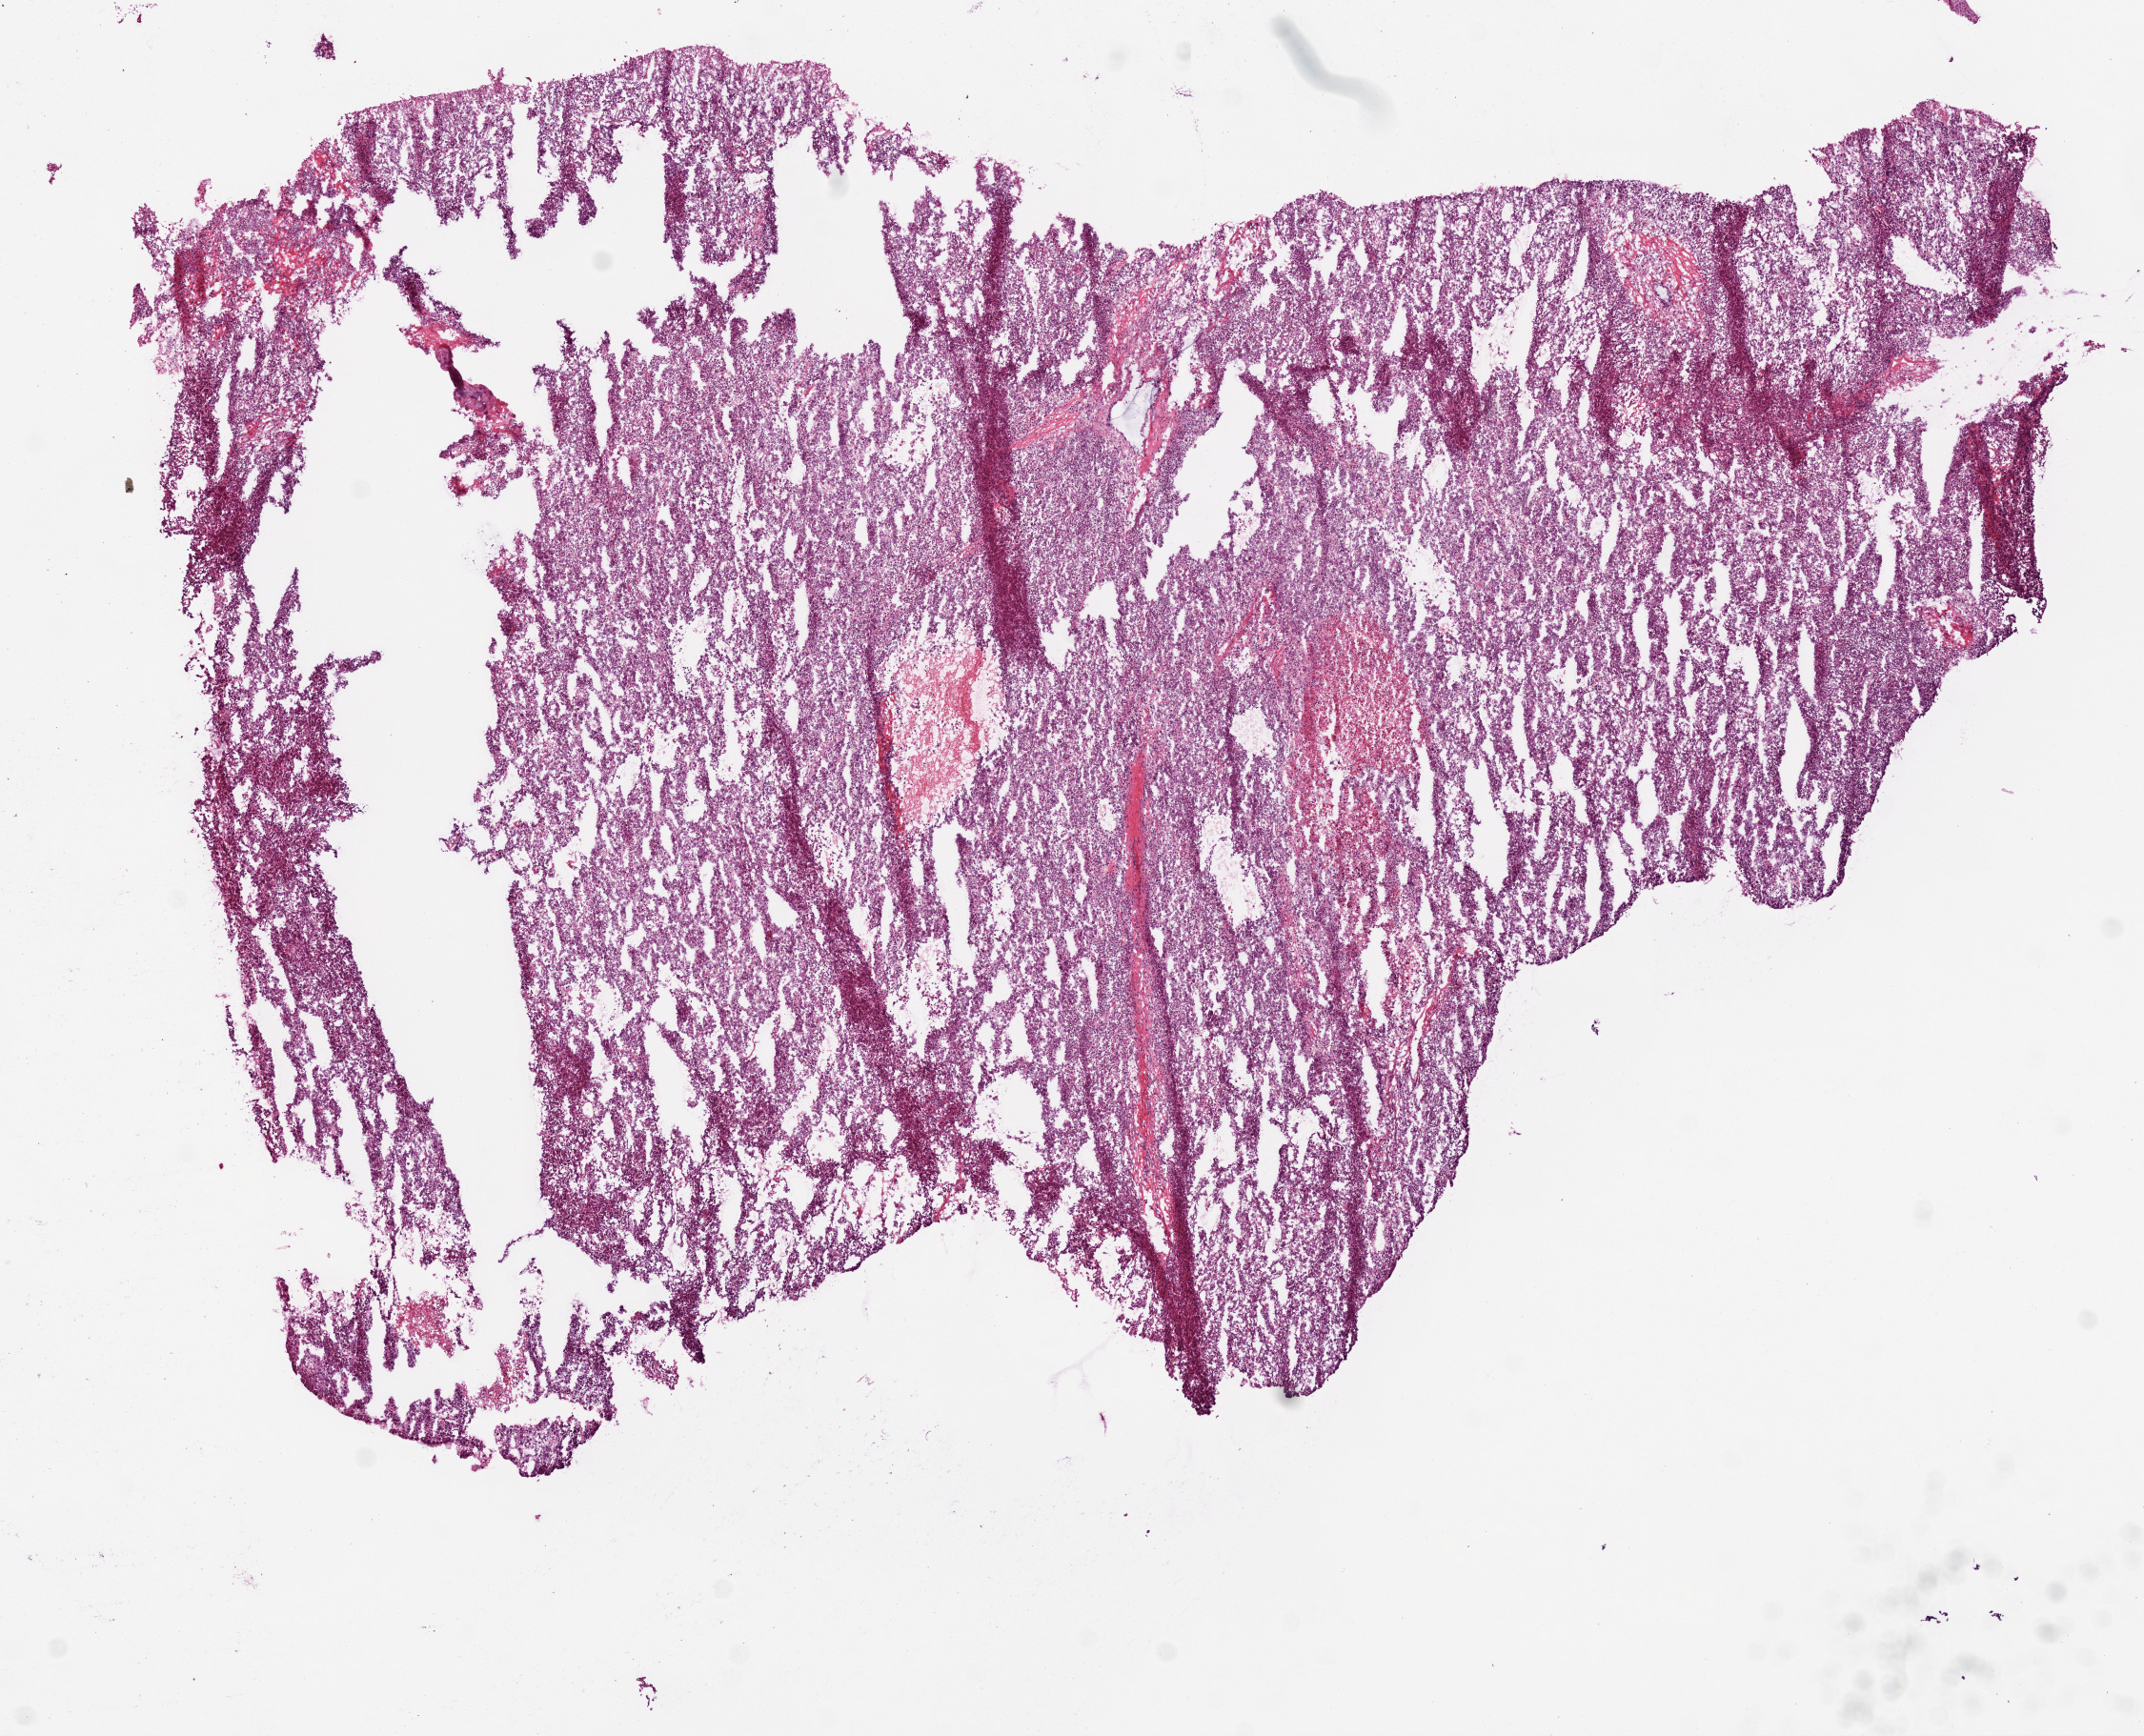
H&E whole-slide image, whole scanned area (about 9.0 x 7.3 mm, slide scanned at 20x) shown as a low-resolution overview; frozen section; primary tumour sample from the lung. Male patient; age at initial diagnosis 56 years. Pathologist review of this section (percent, as recorded): tumour cells 75%, tumour nuclei 75%, normal cells 10%, stromal cells 5%, necrosis 10%.
- laterality: right
- AJCC pathologic stage: IA (7th edition)
- TNM: T1b N0 M0
- diagnosis: Squamous cell carcinoma, NOS (upper lobe, lung)